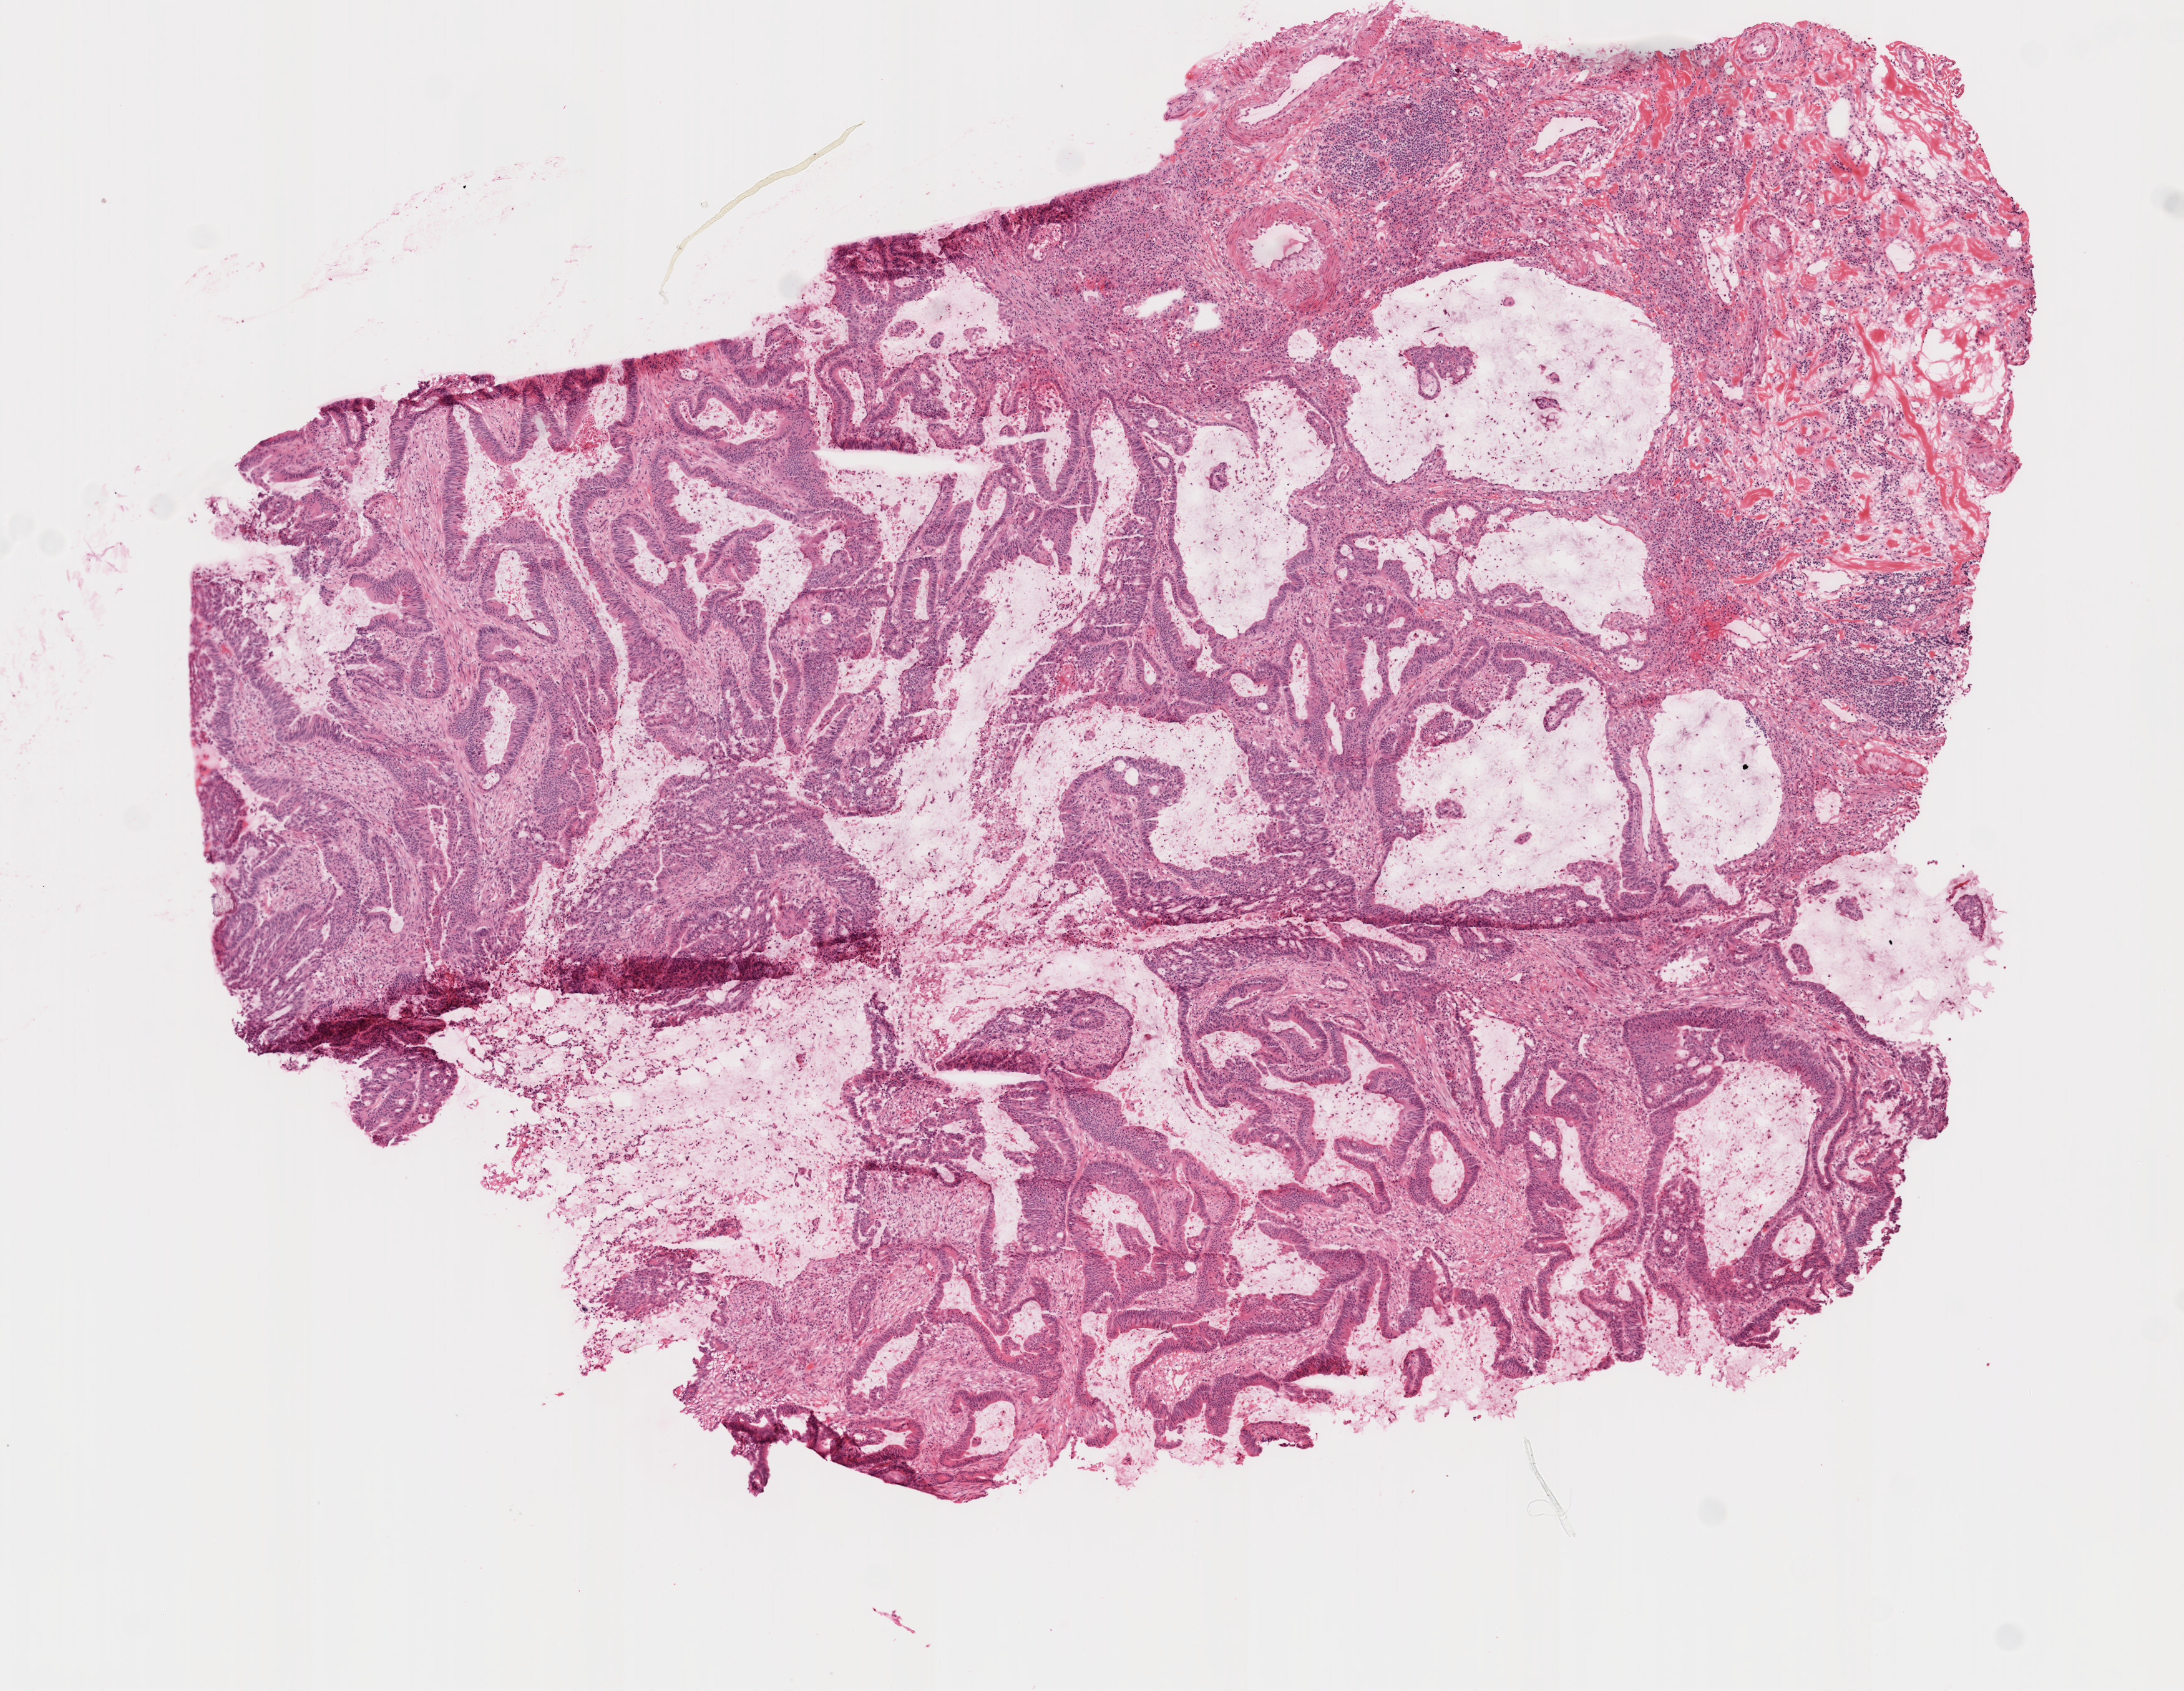
Whole-slide histology image, H&E, shown as a low-resolution overview of the whole scanned area (about 7.0 x 5.4 mm, from a 20x scan); frozen section; sample: primary tumour, colon. Patient: female, age at initial diagnosis 68 years. Composition of this section per pathologist review: tumour cells 80%, tumour nuclei 65%, normal cells 0%, stromal cells 20%, necrosis 0%.
Pathologic diagnosis: Mucinous adenocarcinoma (cecum). AJCC pathologic stage: IIIB (6th edition). Lymph nodes positive (case pathology): 1 of 18 examined.